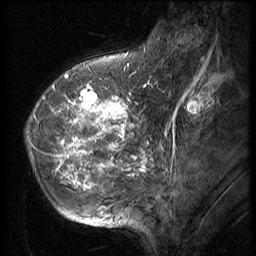
Breast MRI (dynamic contrast-enhanced), one sagittal slice; 3 images stored at this slice position (order not interpretable as contrast timing); 1.5 T; TE 4.2 ms, TR 9 ms; 2.5 mm slice thickness; 256 × 256 image matrix, field of view 180 × 180 mm. Female patient, age 49 years. From the clinical record (not read from this slice): setting: breast cancer imaged before/during neoadjuvant chemotherapy; receptor status: HER2-positive.
Annotated regions visible in this slice (semi-automatic segmentation, software-assisted and operator-edited):
- analysis volume of interest (the breast-tissue region the enhancement analysis was run in; not a lesion): box from (x=25, y=79) to (x=141, y=203) px
- tumour enhancement mask (voxels above the 140 % enhancement threshold inside the analysis volume of interest): (x=26, y=84)–(x=139, y=192)